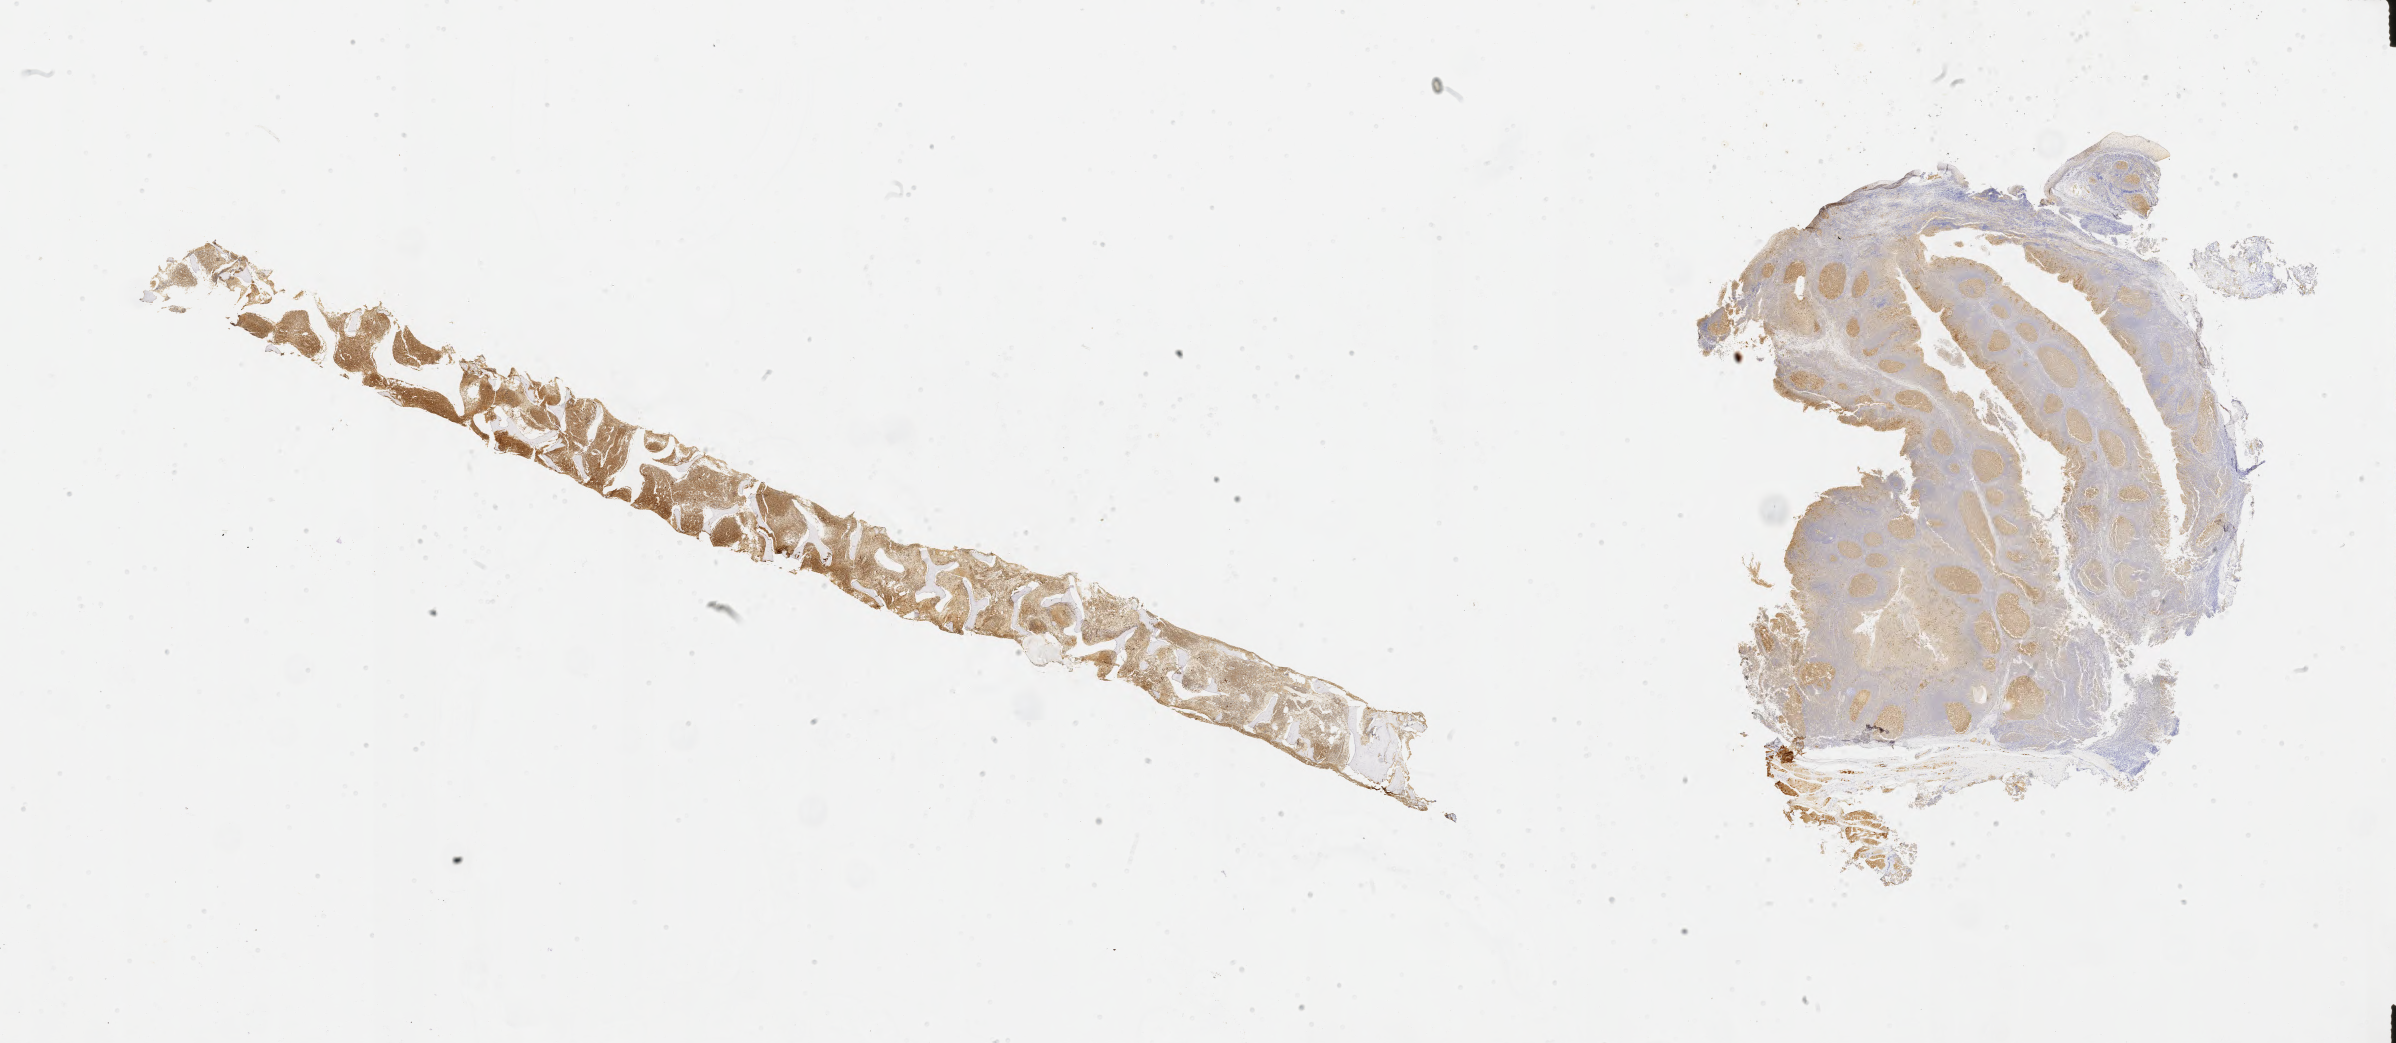
Whole-slide image, immunohistochemical stain for BCL6, a low-resolution overview of the entire scanned area, about 38.7 x 16.9 mm, tumor tissue, anatomic site: bone marrow. Patient: male, age 18 years.
• diagnosis: Burkitt lymphoma, NOS